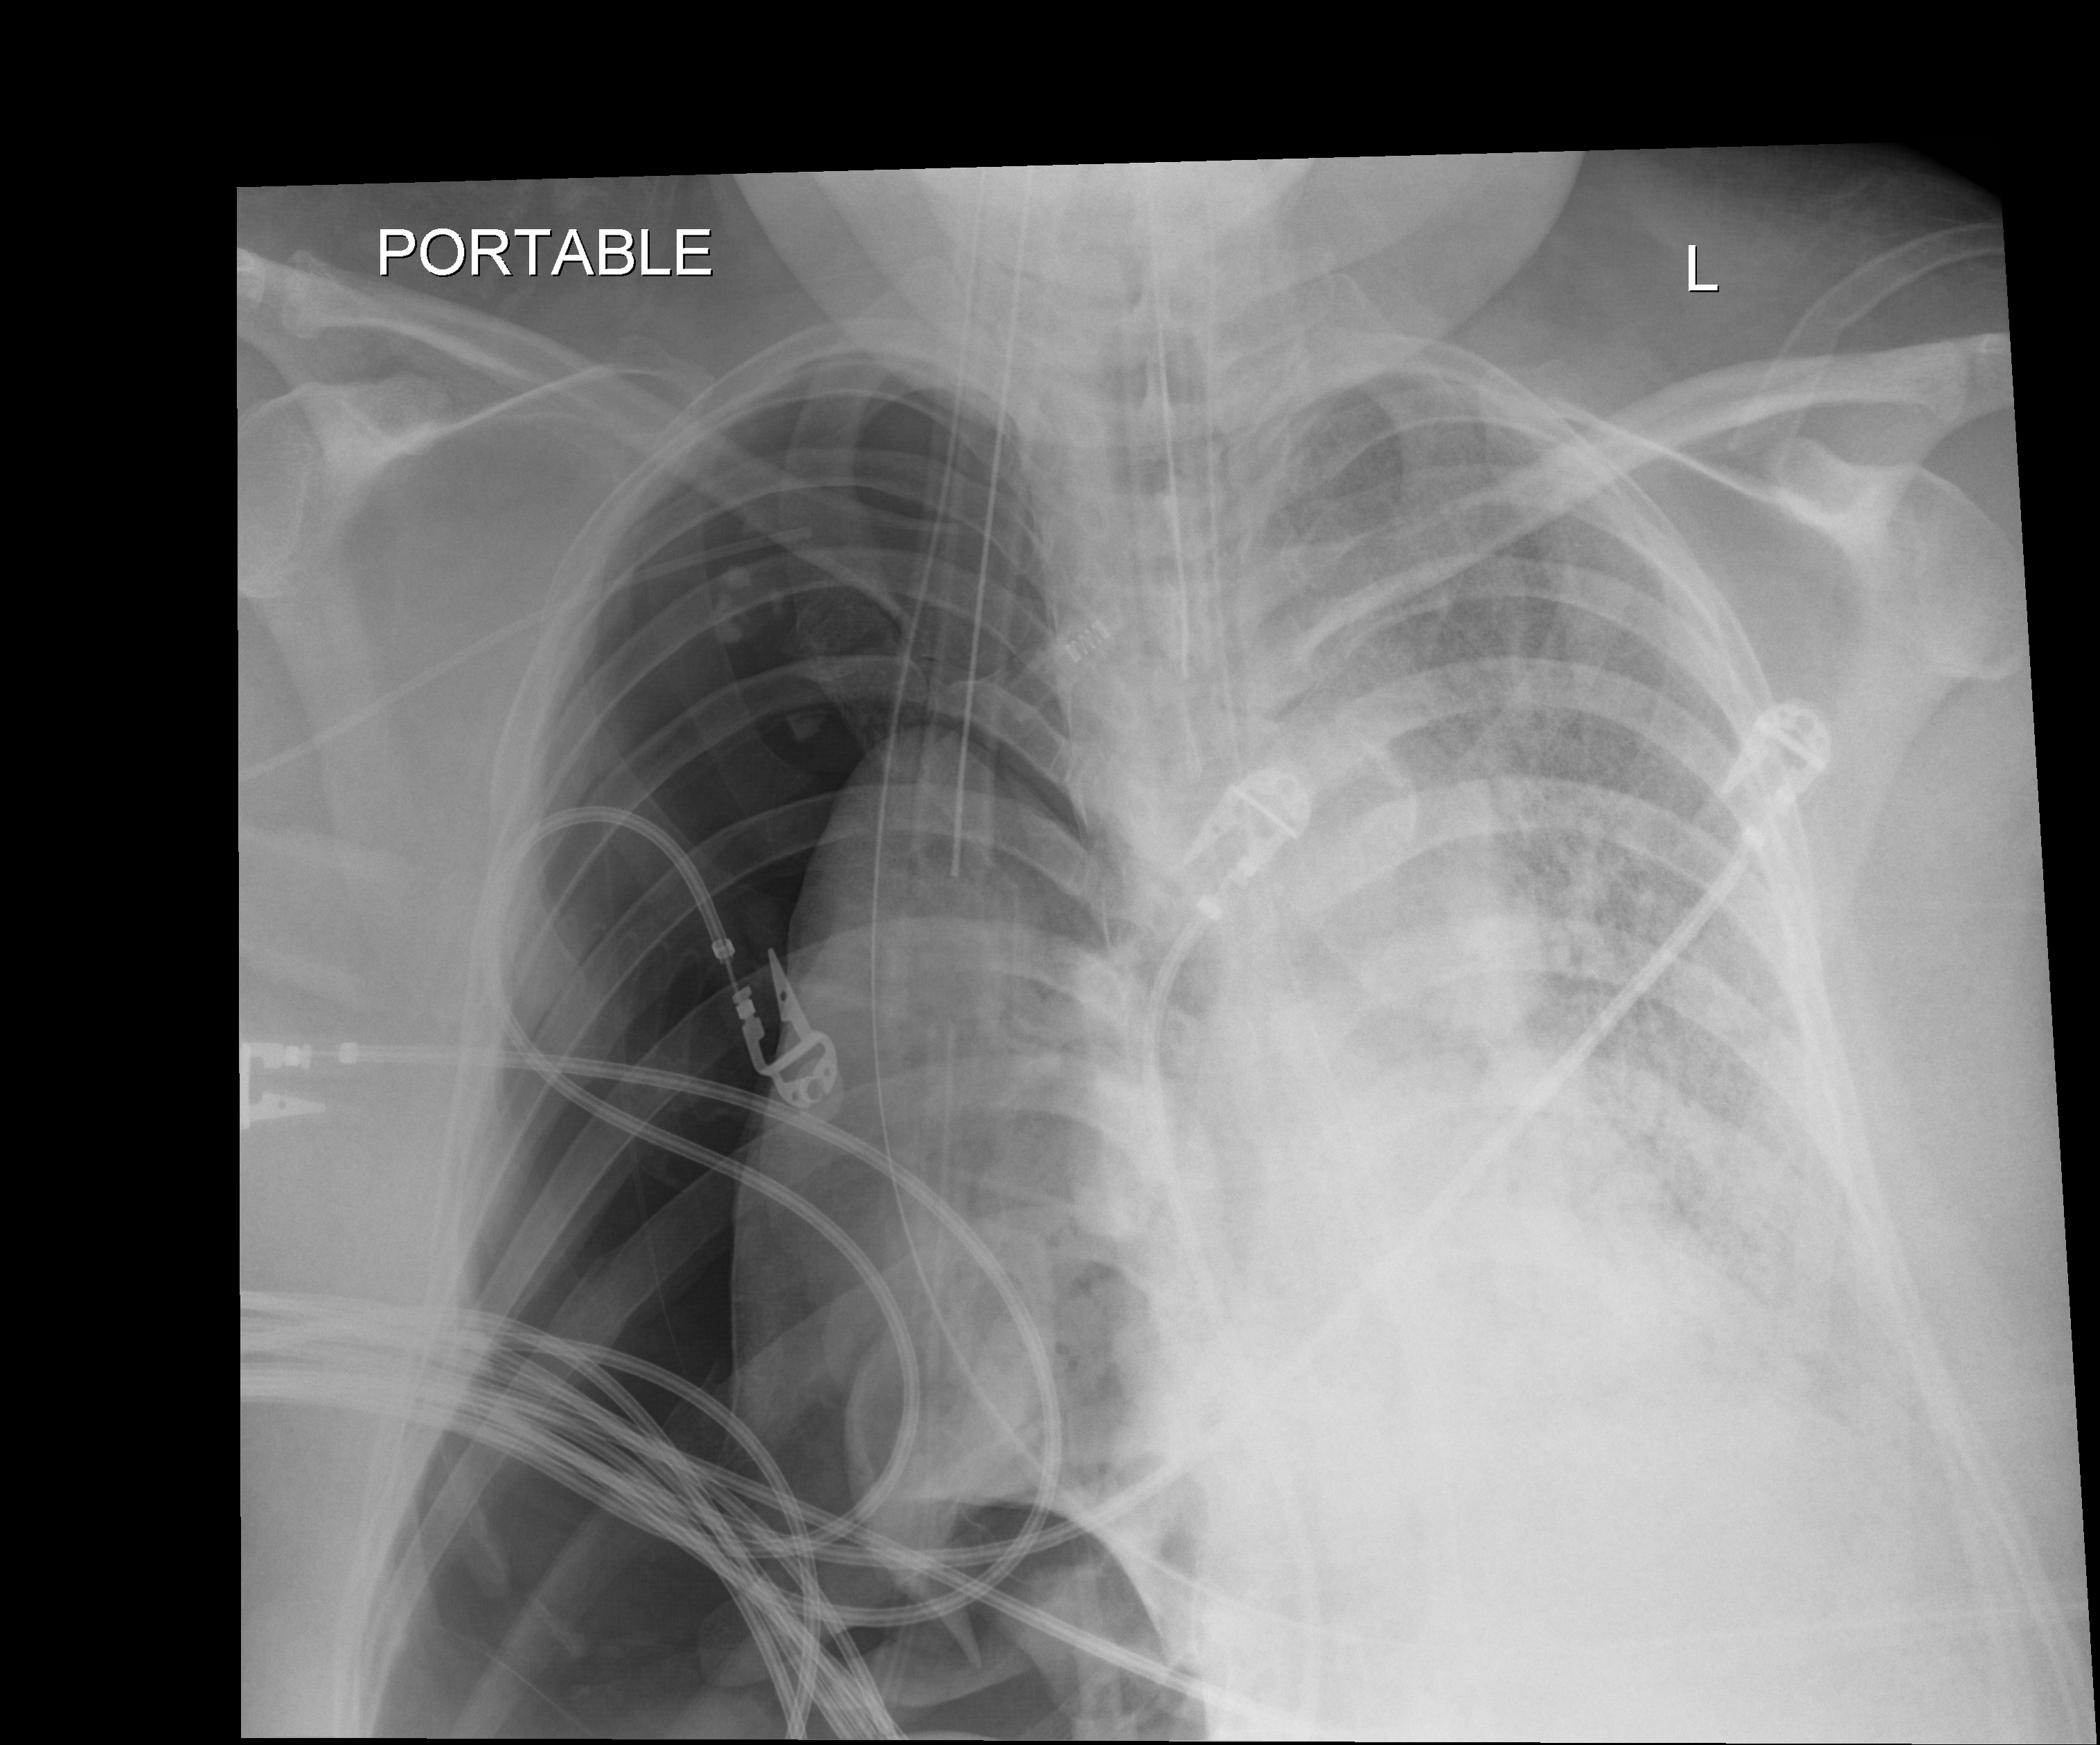
Chest X-ray (portable). Patient hospitalised with COVID-19, aged 18–59 years.
From the hospital-stay record, not from the radiograph (when in the stay this image was taken is not recorded): admitted to intensive care during this hospital stay: yes; chronic kidney disease (admission record): no; mechanically ventilated during this hospital stay: yes.